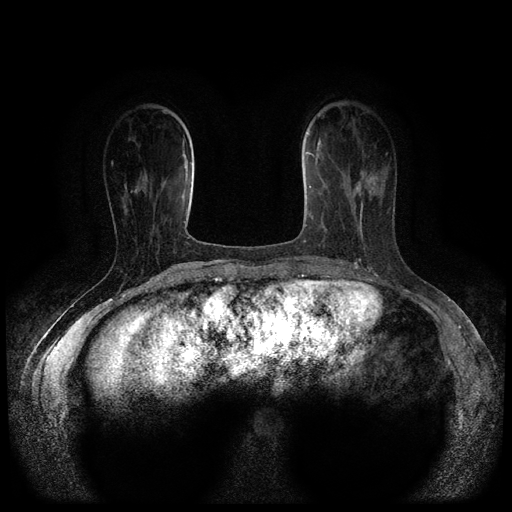
Breast MRI (dynamic contrast-enhanced, multi-phase), one axial slice; slice 29 of 116 in the series (ordered by position); dynamic contrast-enhanced series, time point 2 of 5 at this slice position (early post-contrast); 1.5 T; TE 2.6 ms, TR 5.4 ms; 2 mm slice thickness; 512 × 512 image matrix. Patient: female, 47 years.
Structures marked on this image (semi-automatic segmentation, software-assisted and operator-edited):
- breast lesion (labelled 'tumour' in the annotation; benign lesions carry a separate 'benign' label): box from (x=354, y=179) to (x=363, y=194) px